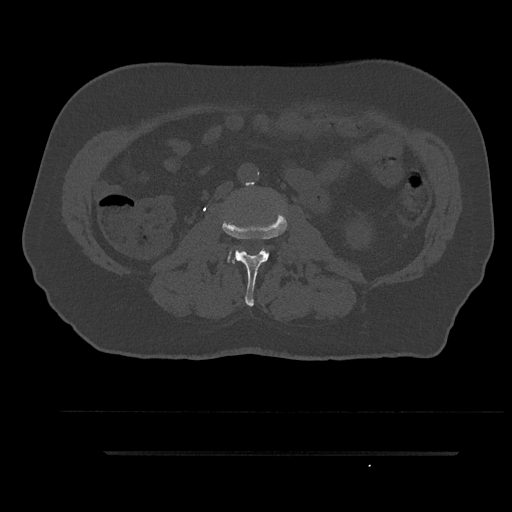
CT including the spine, one axial slice; position 88 of 797 along the scan axis; 120 kVp; bone window (W 1800 / L 400 HU); 0.5 mm slice thickness; 512 × 512 image matrix, field of view 432 × 432 mm. Male patient, age 63 years. From the clinical record (not read from this slice): primary cancer: renal; vertebrae with lytic lesions (as recorded): T8.
Annotated regions visible in this slice (semi-automatic segmentation, software-assisted and operator-edited):
- L2 vertebra: bounding box [x1, y1, x2, y2] px = [222, 211, 287, 307]
- L3 vertebra: [227, 252, 231, 262]